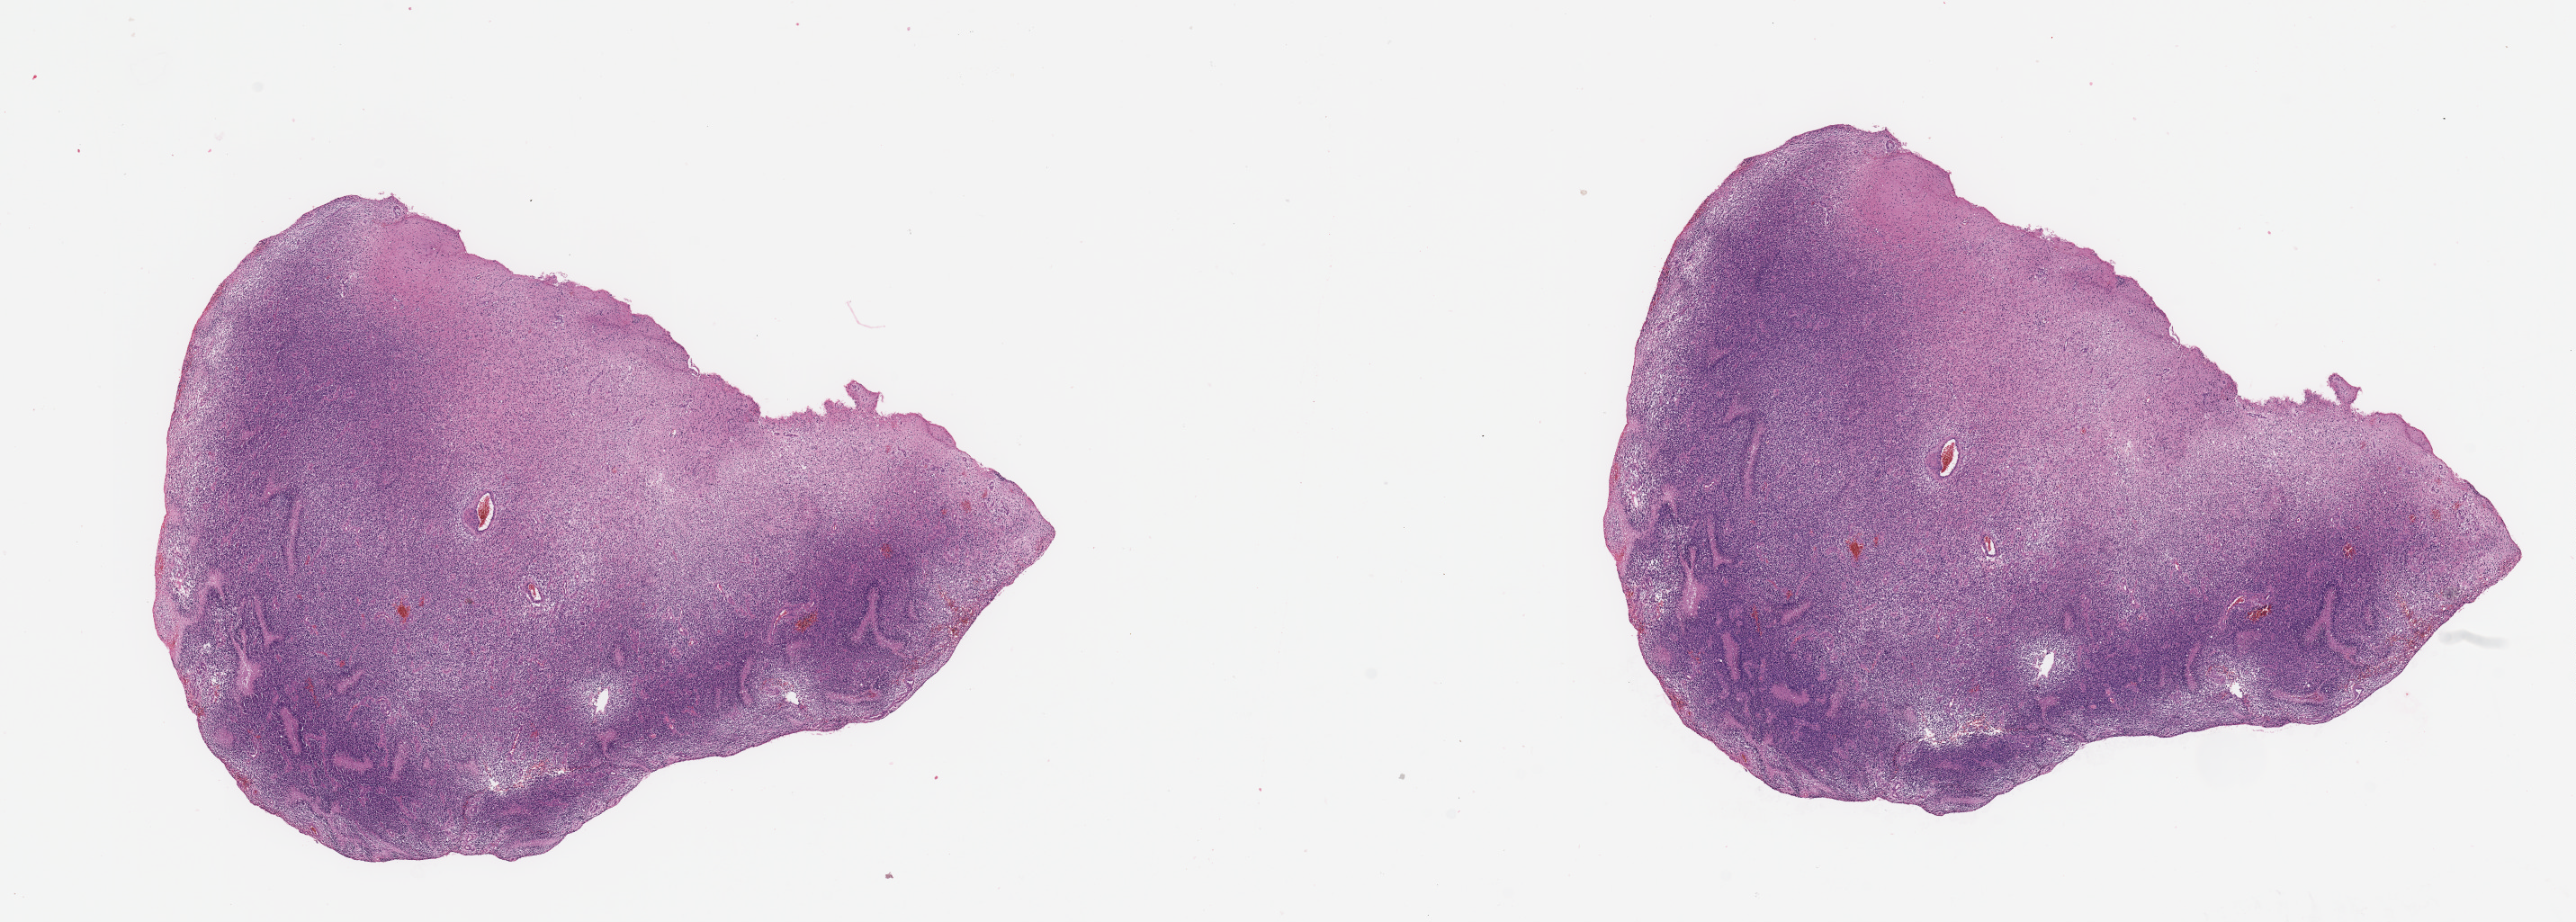
Whole-slide histology image, H&E — a low-resolution overview of the entire scanned area, about 22.6 x 8.1 mm (from a 20x scan), brain, tumour tissue. Female, 68 y/o.
Diagnosis: Glioblastoma. Primary tumour site (as recorded): parietal lobe.